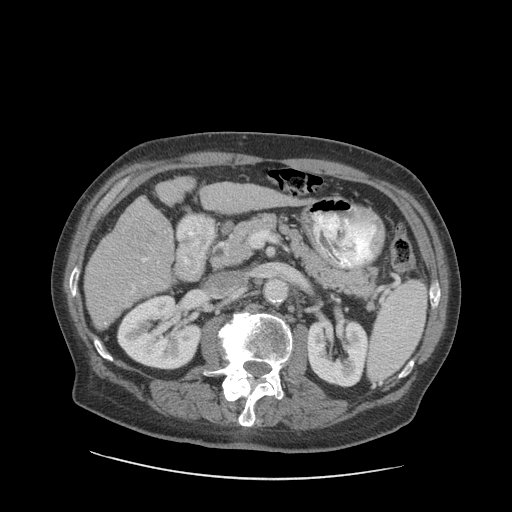
Contrast-enhanced abdominal CT (liver protocol), one axial slice; slice 40 of 89 in the series (ordered by position); reconstruction kernel STANDARD; soft-tissue window (W 400 / L 40 HU); 512 × 512 image matrix, field of view 420 × 420 mm. Case-level facts recorded for this patient, not image findings: diagnosis: hepatocellular carcinoma (patient treated with transarterial chemoembolisation; whether this scan precedes or follows treatment is not stated here); TNM stage (as recorded): Stage-I; Child-Pugh class: A; tumour differentiation: moderately differentiated; tumour nodularity: uninodular.
Structures marked on this image (semi-automatic segmentation, software-assisted and operator-edited):
- liver parenchyma outside the tumour (the mass and vessels are separate outlines, so this box may not span the whole liver): bounding box <84,184,290,328> (left, top, right, bottom; pixels)
- mass: <124,209,168,274>
- liver vessels: <111,261,159,310>